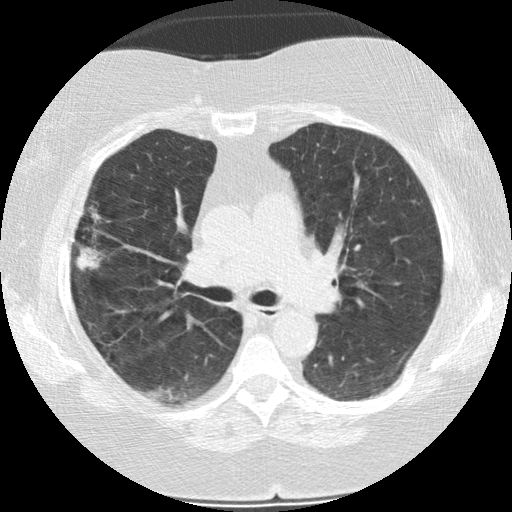
Low-dose screening chest CT, axial slice; baseline annual screen; lung window (W 1500 / L -600 HU); 2.5 mm slice thickness; 120 kVp; slice 76 of 187 in the series. Female, age 73 years at enrolment. Former smoker at enrolment.
Lesion marked by an expert reader, bounding box (x1, y1, x2, y2) in pixels: (58, 213, 113, 277). Reader record for this screening exam (exam-level; its link to the box is not recorded): non-calcified nodule or mass ≥4 mm, right upper lobe, 21 × 14 mm, poorly defined margins, soft tissue attenuation. Participant outcome: lung cancer diagnosed 482 days after this screen (after the second annual screen) — bronchiolo-alveolar adenocarcinoma, NOS, right upper lobe, moderately differentiated (G2), stage IIIB (AJCC 6th edition), 21 mm at pathology.